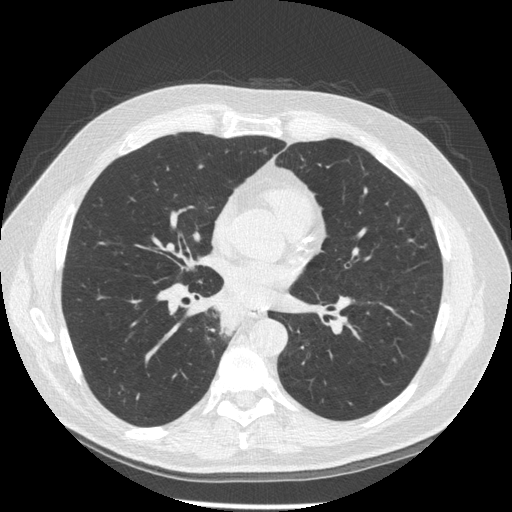
Low-dose screening chest CT, axial slice, third screening round (two years after baseline), lung window (W 1500 / L -600 HU), 120 kVp, 512 × 512 image matrix, field of view 370 × 370 mm. Male participant, aged 61 years at enrolment. Former smoker at enrolment.
- Lesion marked by an expert reader, bounding box <201,298,255,350> (left, top, right, bottom; pixels).
- No non-calcified nodule or mass ≥4 mm was recorded by the screening reader at this exam.
- Official screen result: positive, other.